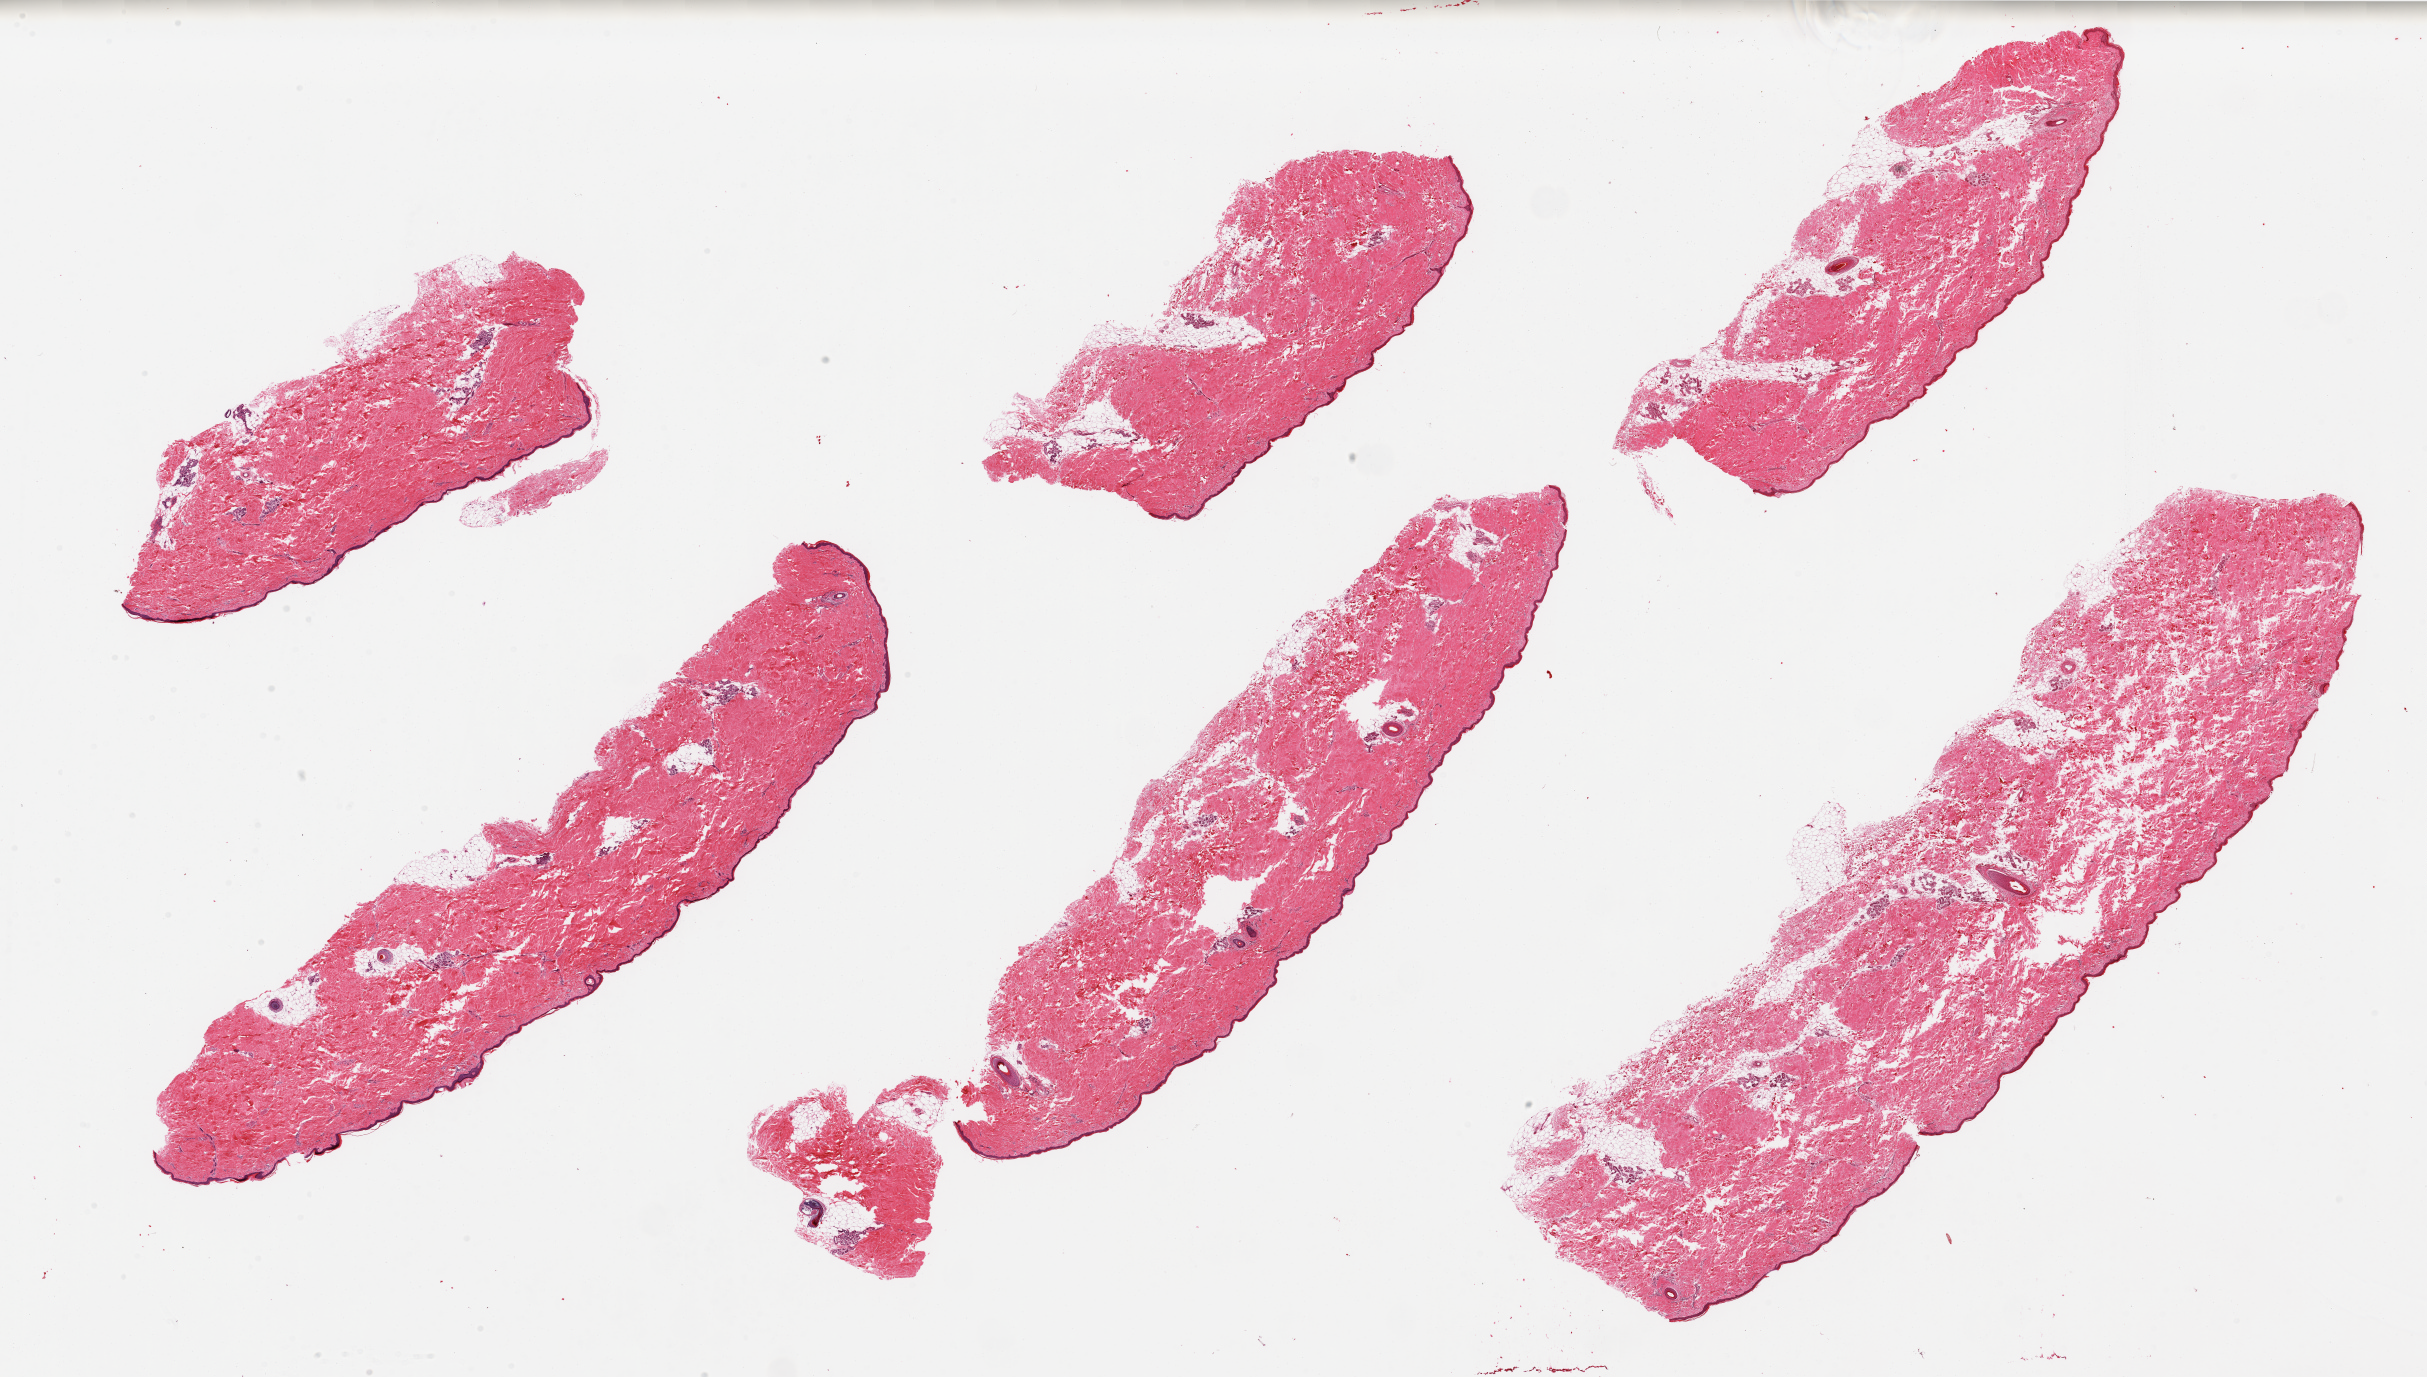
Haematoxylin and eosin whole-slide image, a low-resolution overview of the entire scanned area, about 38.4 x 21.8 mm, PAXgene-fixed, paraffin-embedded tissue, target tissue: skin of lower leg, donor tissue sample. Donor sex: male.
• review note (as recorded): 6 pieces, minimal dermal fat; squamous epithelium is 35-50 microns